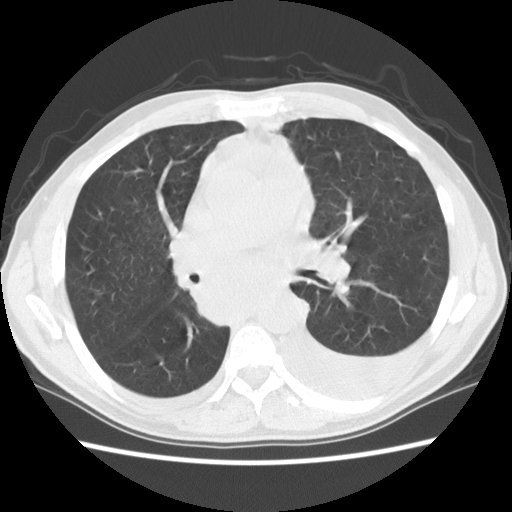
Axial slice from a low-dose chest CT screening exam; baseline annual screen; lung window (W 1500 / L -600 HU); 2.5 mm slice thickness; 140 kVp; slice 53 of 135 in the series. Male participant, aged 60 years at enrolment.
Lesion marked by an expert reader, bounding box <176,239,300,330> (left, top, right, bottom; pixels). No non-calcified nodule or mass ≥4 mm was recorded by the screening reader at this exam. Official screen result: negative screen, significant abnormalities not suspicious for lung cancer. Lung cancer was diagnosed 12 days after this screen: squamous cell carcinoma, NOS, carina, poorly differentiated (G3), stage IV (AJCC 6th edition).